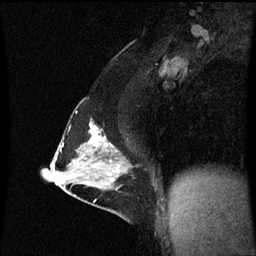
Breast MRI (dynamic contrast-enhanced), one sagittal slice. Slice 34 of 60 in the series (ordered by position). Dynamic contrast-enhanced series, image 2 of 3 at this slice position (ordered by acquisition). 1.5 T. TE 4.2 ms, TR 8.9 ms. 2 mm slice thickness. 256 × 256 image matrix. Patient: female, 47 years. From the clinical record (not read from this slice): setting: breast cancer imaged before/during neoadjuvant chemotherapy; receptor status: HR-positive, HER2-negative.
Outlined on this slice (semi-automatically segmented with operator editing):
- analysis volume of interest (the breast-tissue region the enhancement analysis was run in; not a lesion): bounding box [x1, y1, x2, y2] px = [53, 110, 135, 209]
- tumour enhancement mask (voxels above the 70 % enhancement threshold inside the analysis volume of interest): [89, 124, 120, 167]